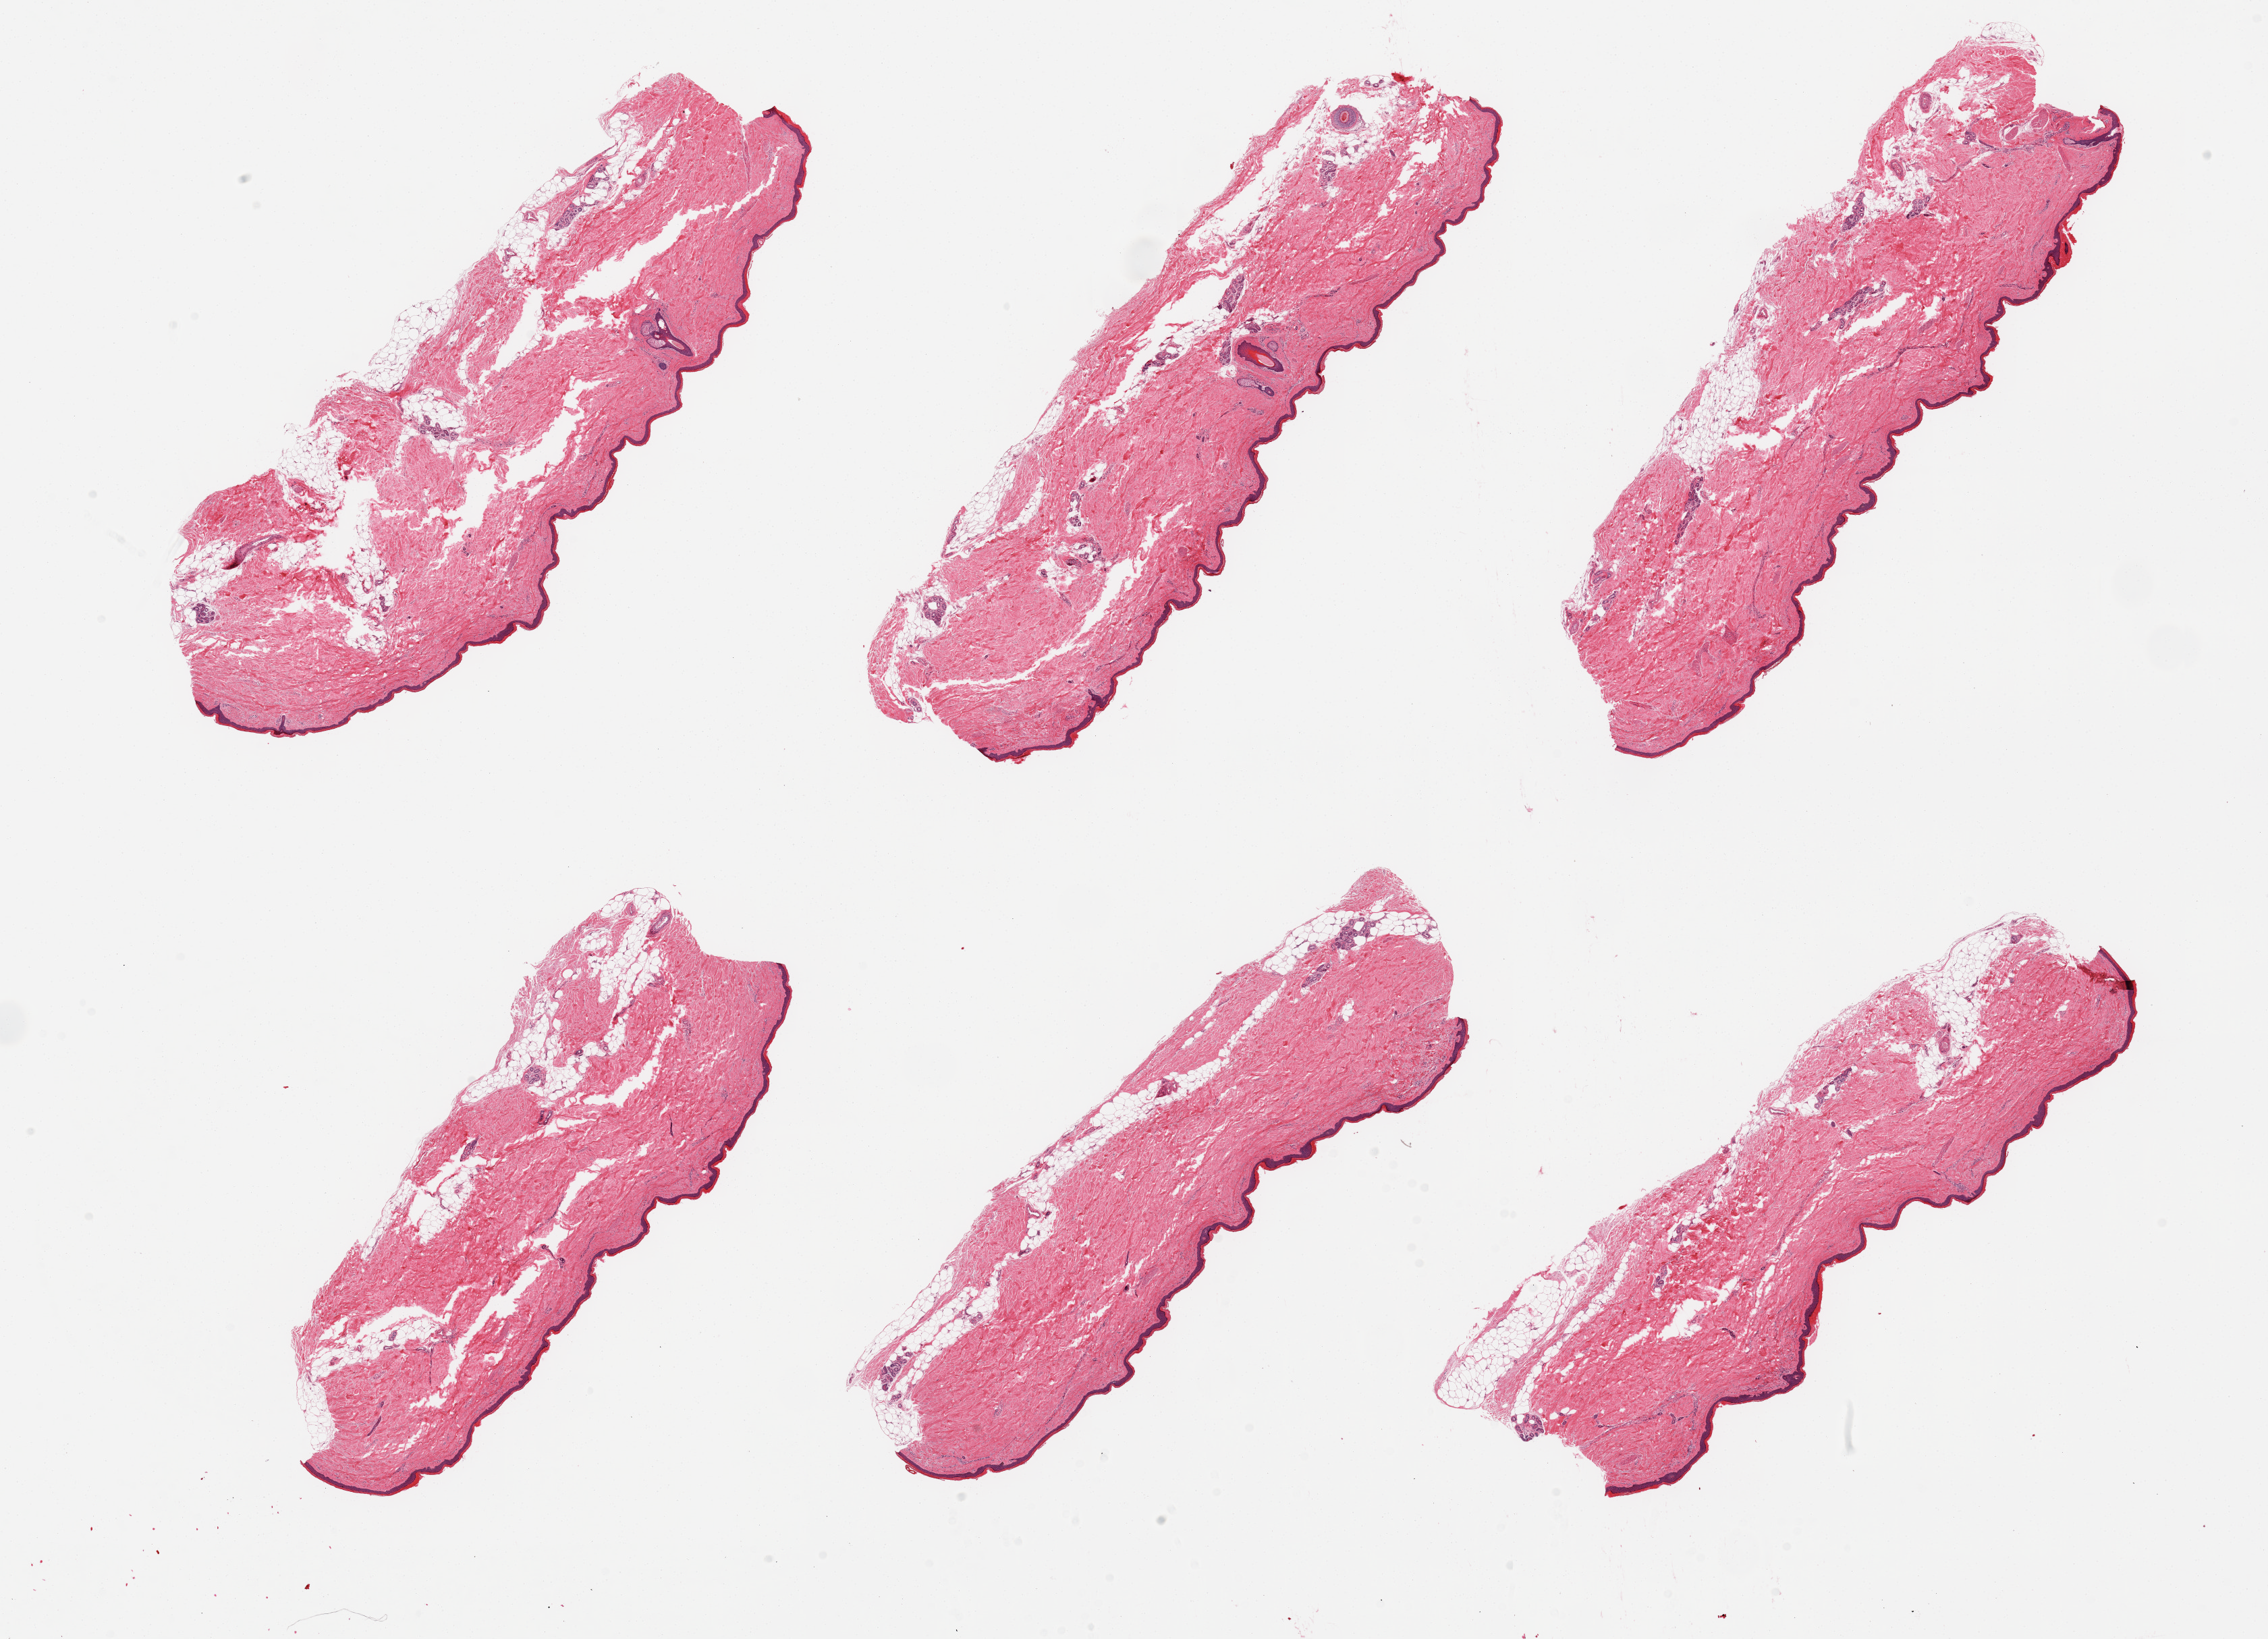
Digitized haematoxylin and eosin-stained section, brightfield — whole scanned area (about 26.6 x 19.2 mm, from a 20x scan) shown as a low-resolution overview; PAXgene-fixed, paraffin-embedded tissue; sampled site (target tissue): skin of lower leg; donor tissue sample.
Pathologist's review note for this sample: 6 pieces; well trimmed; 20% intradermal fat.